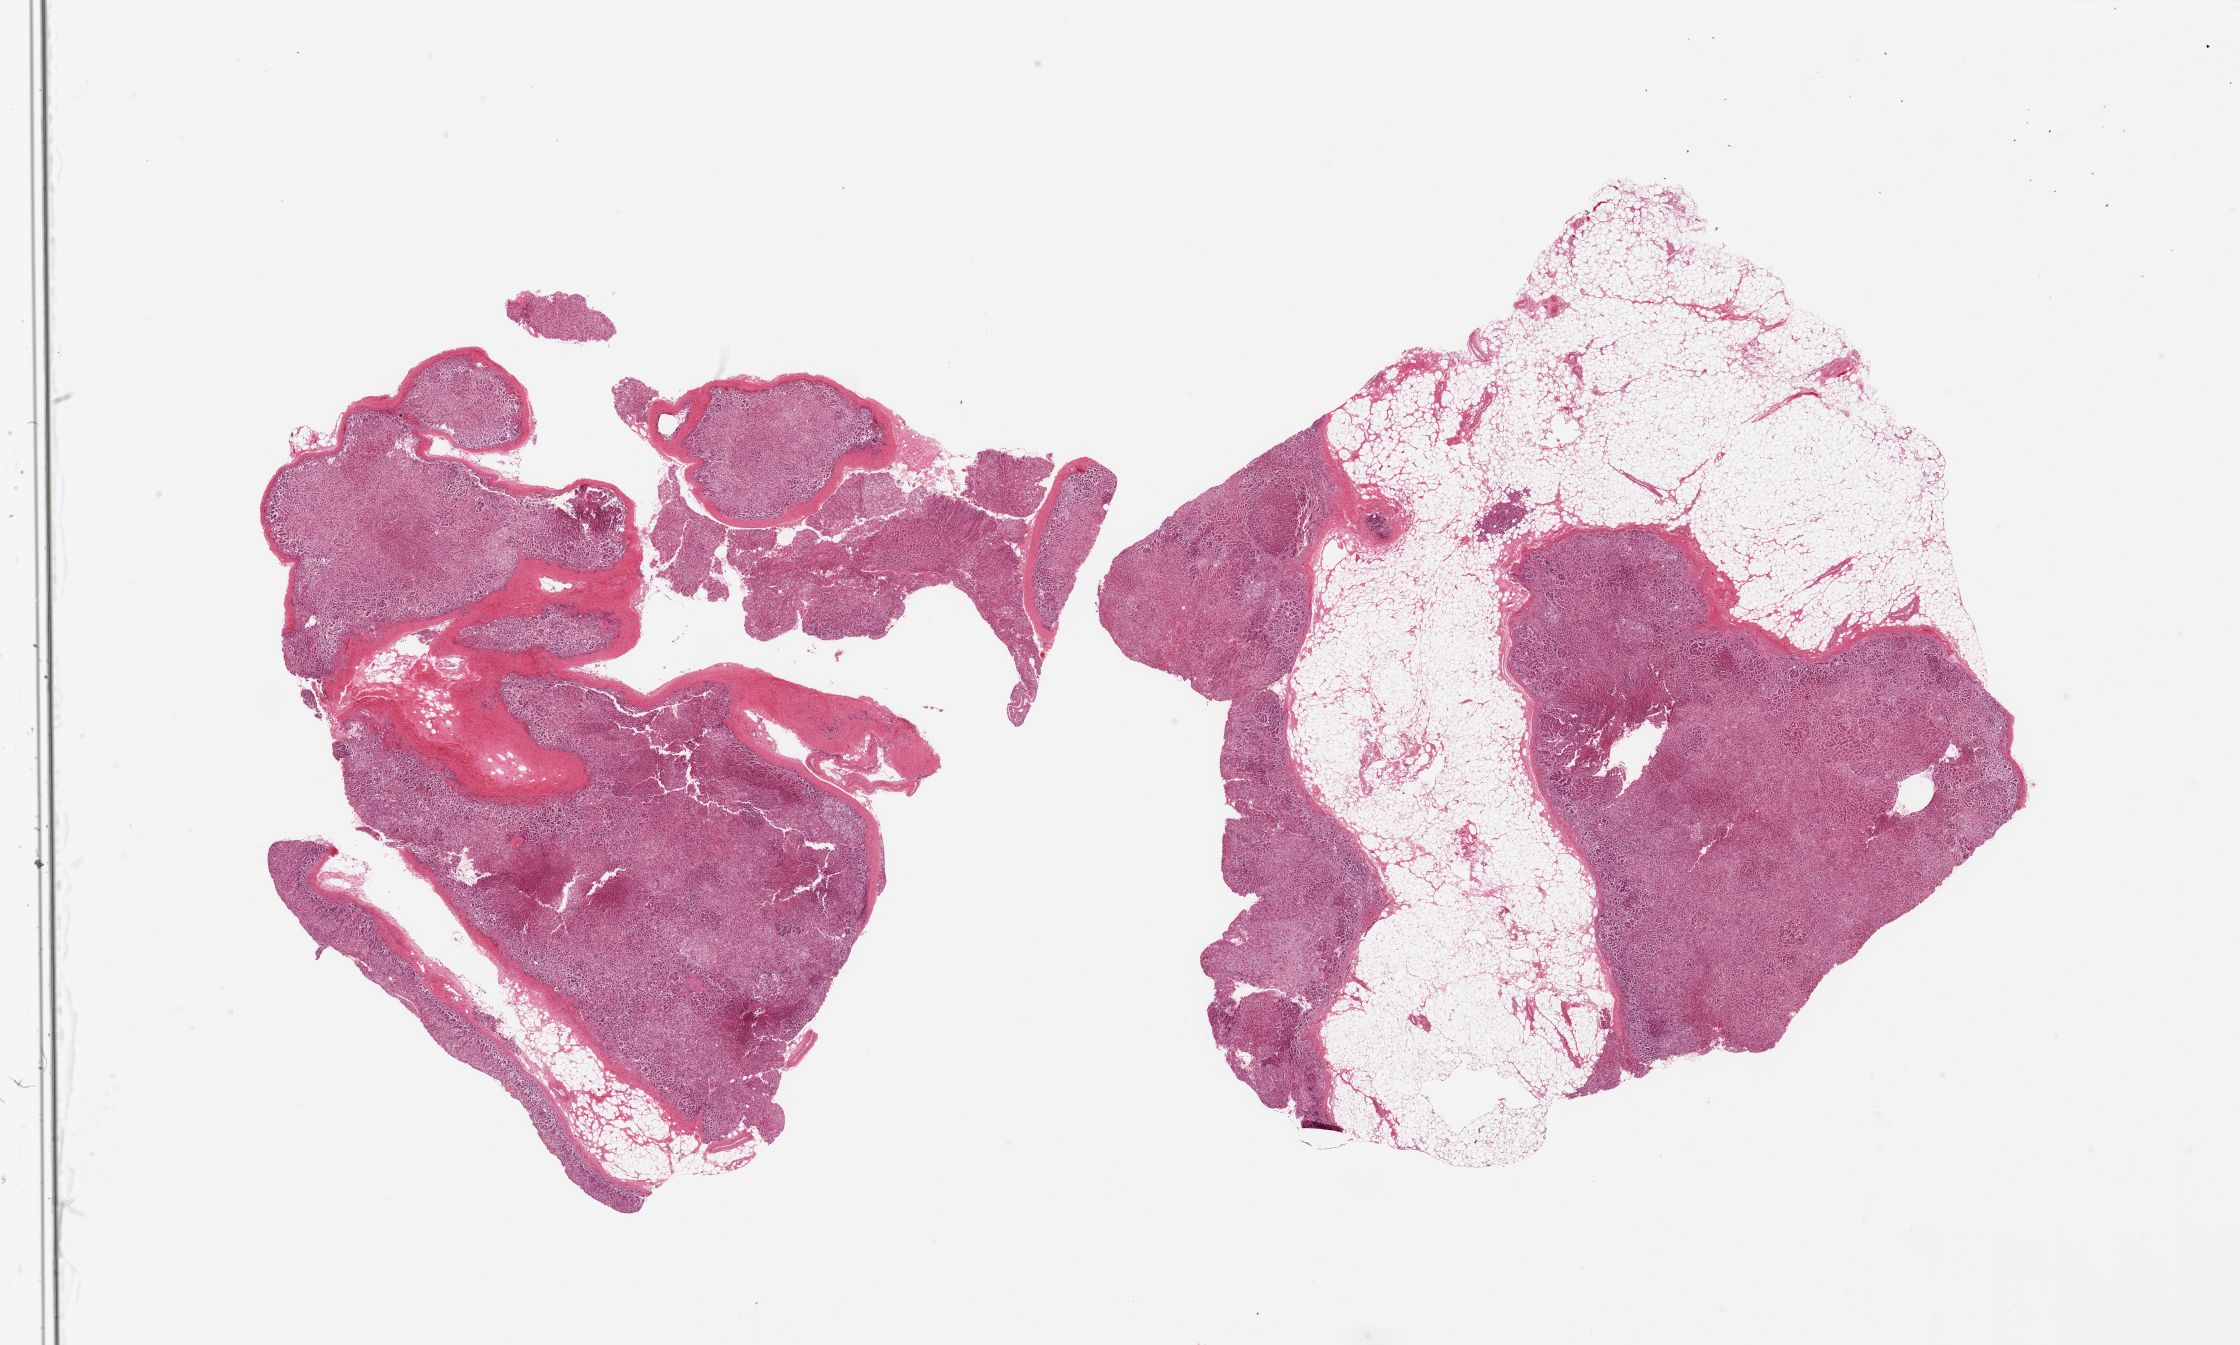
H&E whole-slide image, shown as a low-resolution overview of the whole scanned area (about 35.4 x 21.3 mm), PAXgene-fixed paraffin-embedded (PFPE) section, section of adrenal gland (target tissue), donor tissue sample. Donor sex: male.
Reviewer comment on this tissue sample: 2 pieces, 1 has 50% fat.